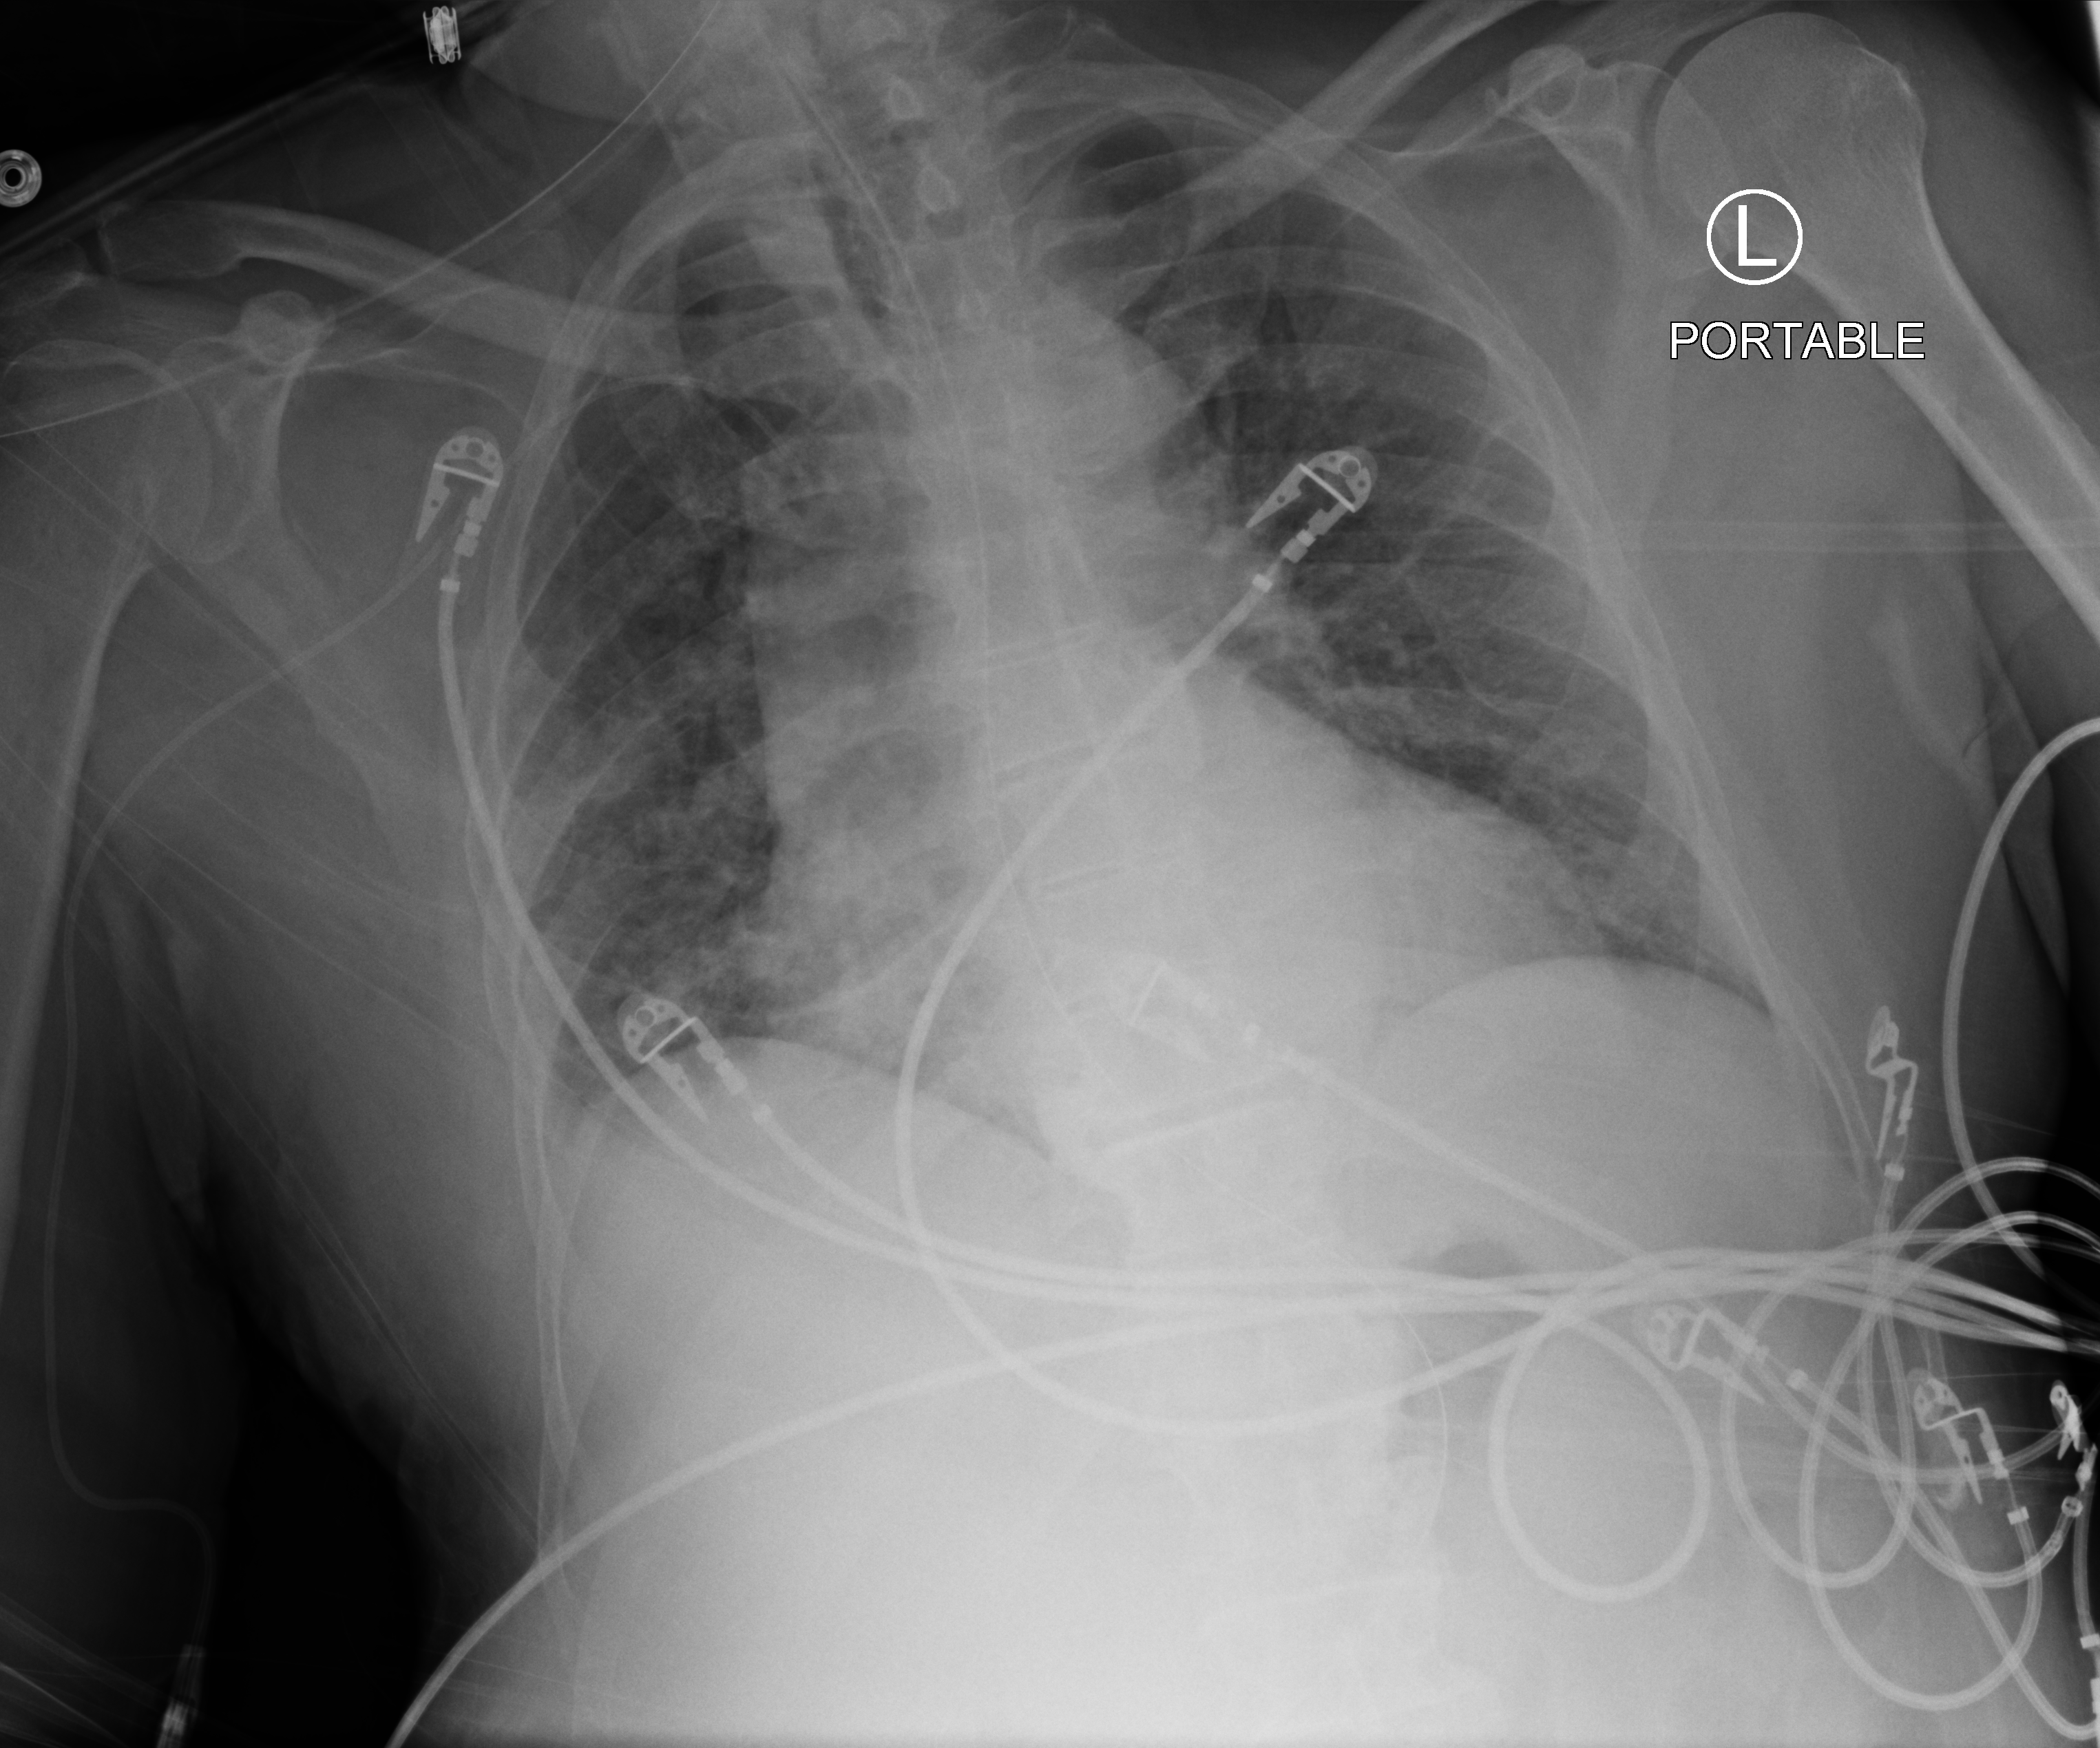
Bedside chest radiograph (computed radiography); anteroposterior (AP) projection. Male patient hospitalised with COVID-19, age 60–74 years.
From the hospital-stay record, not from the radiograph (when in the stay this image was taken is not recorded):
- chronic kidney disease (admission record): no